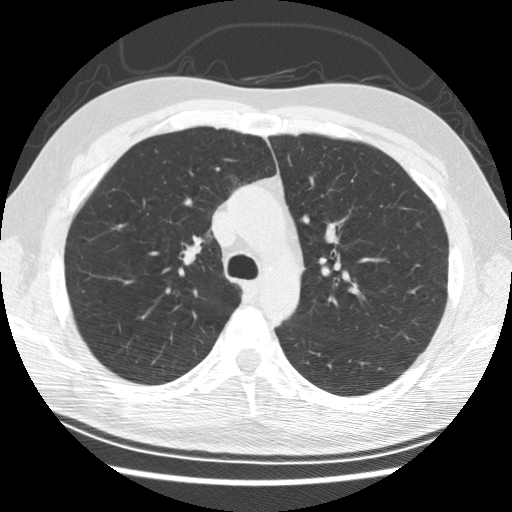
Axial slice from a low-dose chest CT screening exam. Baseline annual screen. Lung window (W 1500 / L -600 HU). 2.5 mm slice thickness. Standard (soft-tissue) reconstruction kernel (STANDARD). 120 kVp. 512 × 512 image matrix, field of view 340 × 340 mm. Male, age 57 years at enrolment.
Expert-annotated lung lesion, box from (x=164, y=221) to (x=223, y=278) px. The screening reader recorded 6 non-calcified nodules or masses ≥4 mm on this exam; which of them this box marks is not recorded. Official screen result: negative screen, minor abnormalities not suspicious for lung cancer.